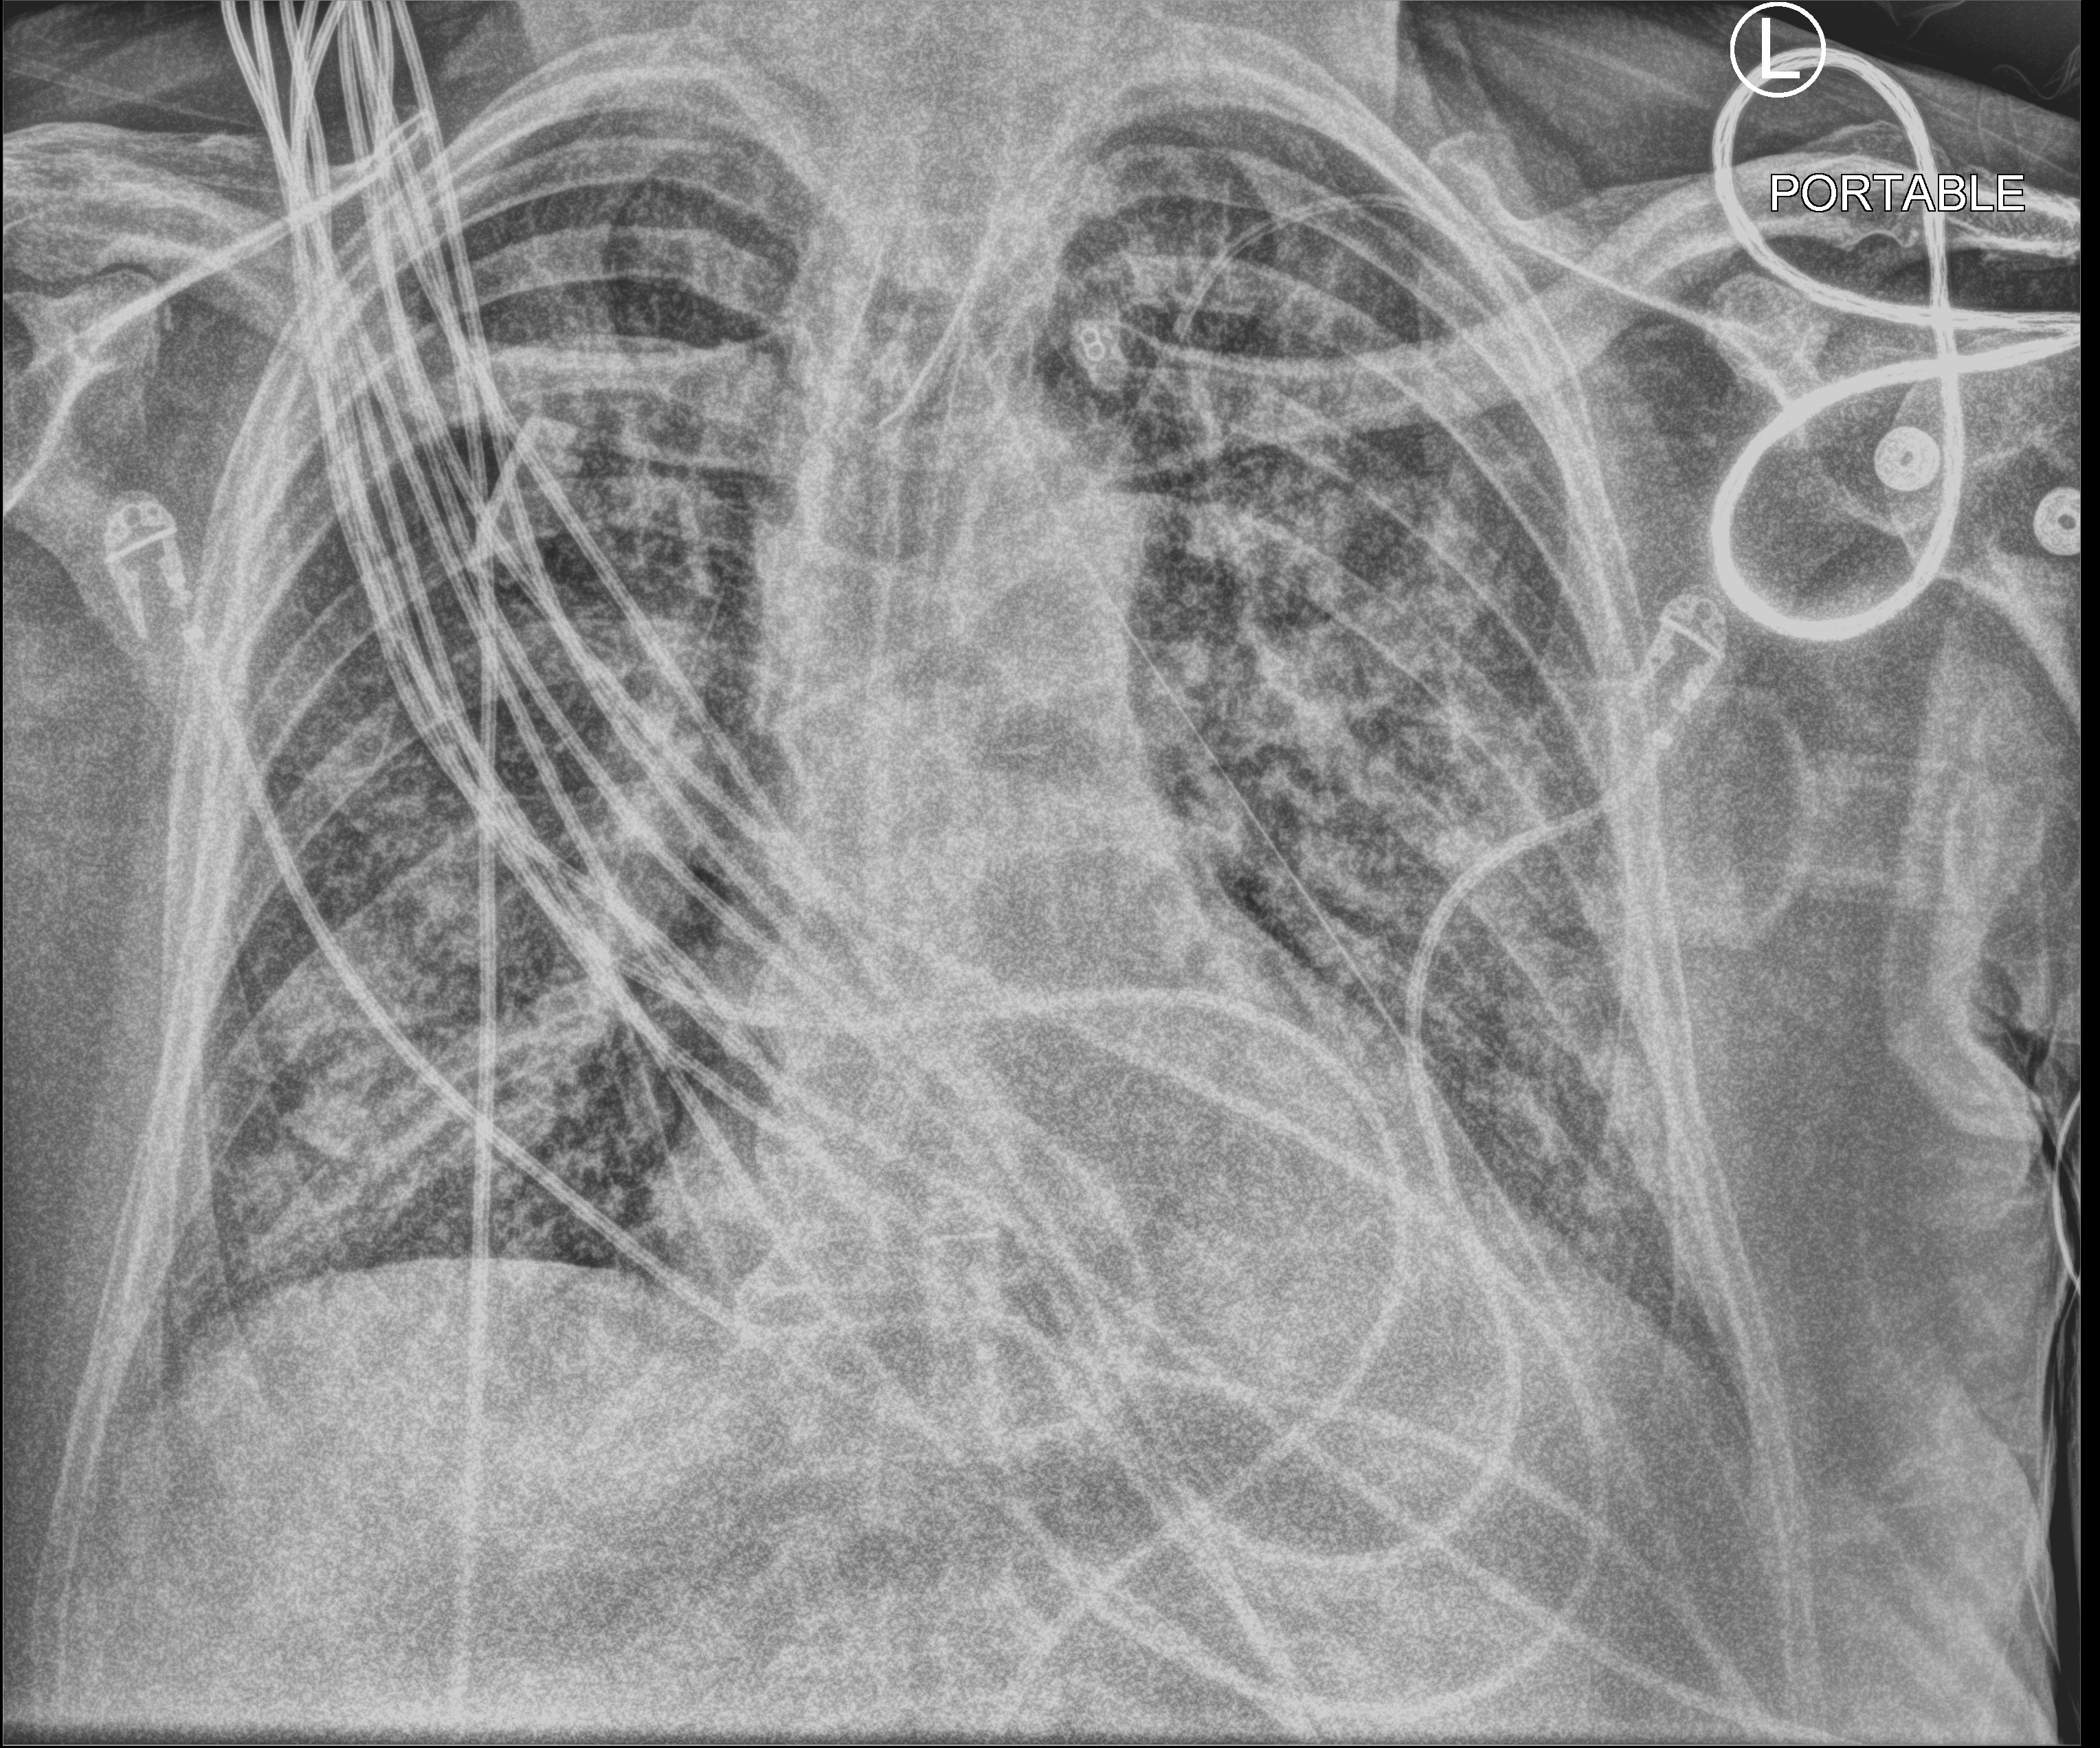
Chest X-ray (portable); anteroposterior (AP) projection. Patient hospitalised with COVID-19; male, aged 75–90 years.
From the hospital-stay record, not from the radiograph (when in the stay this image was taken is not recorded):
- other chronic lung disease (admission record): no
- mechanically ventilated during this hospital stay: yes